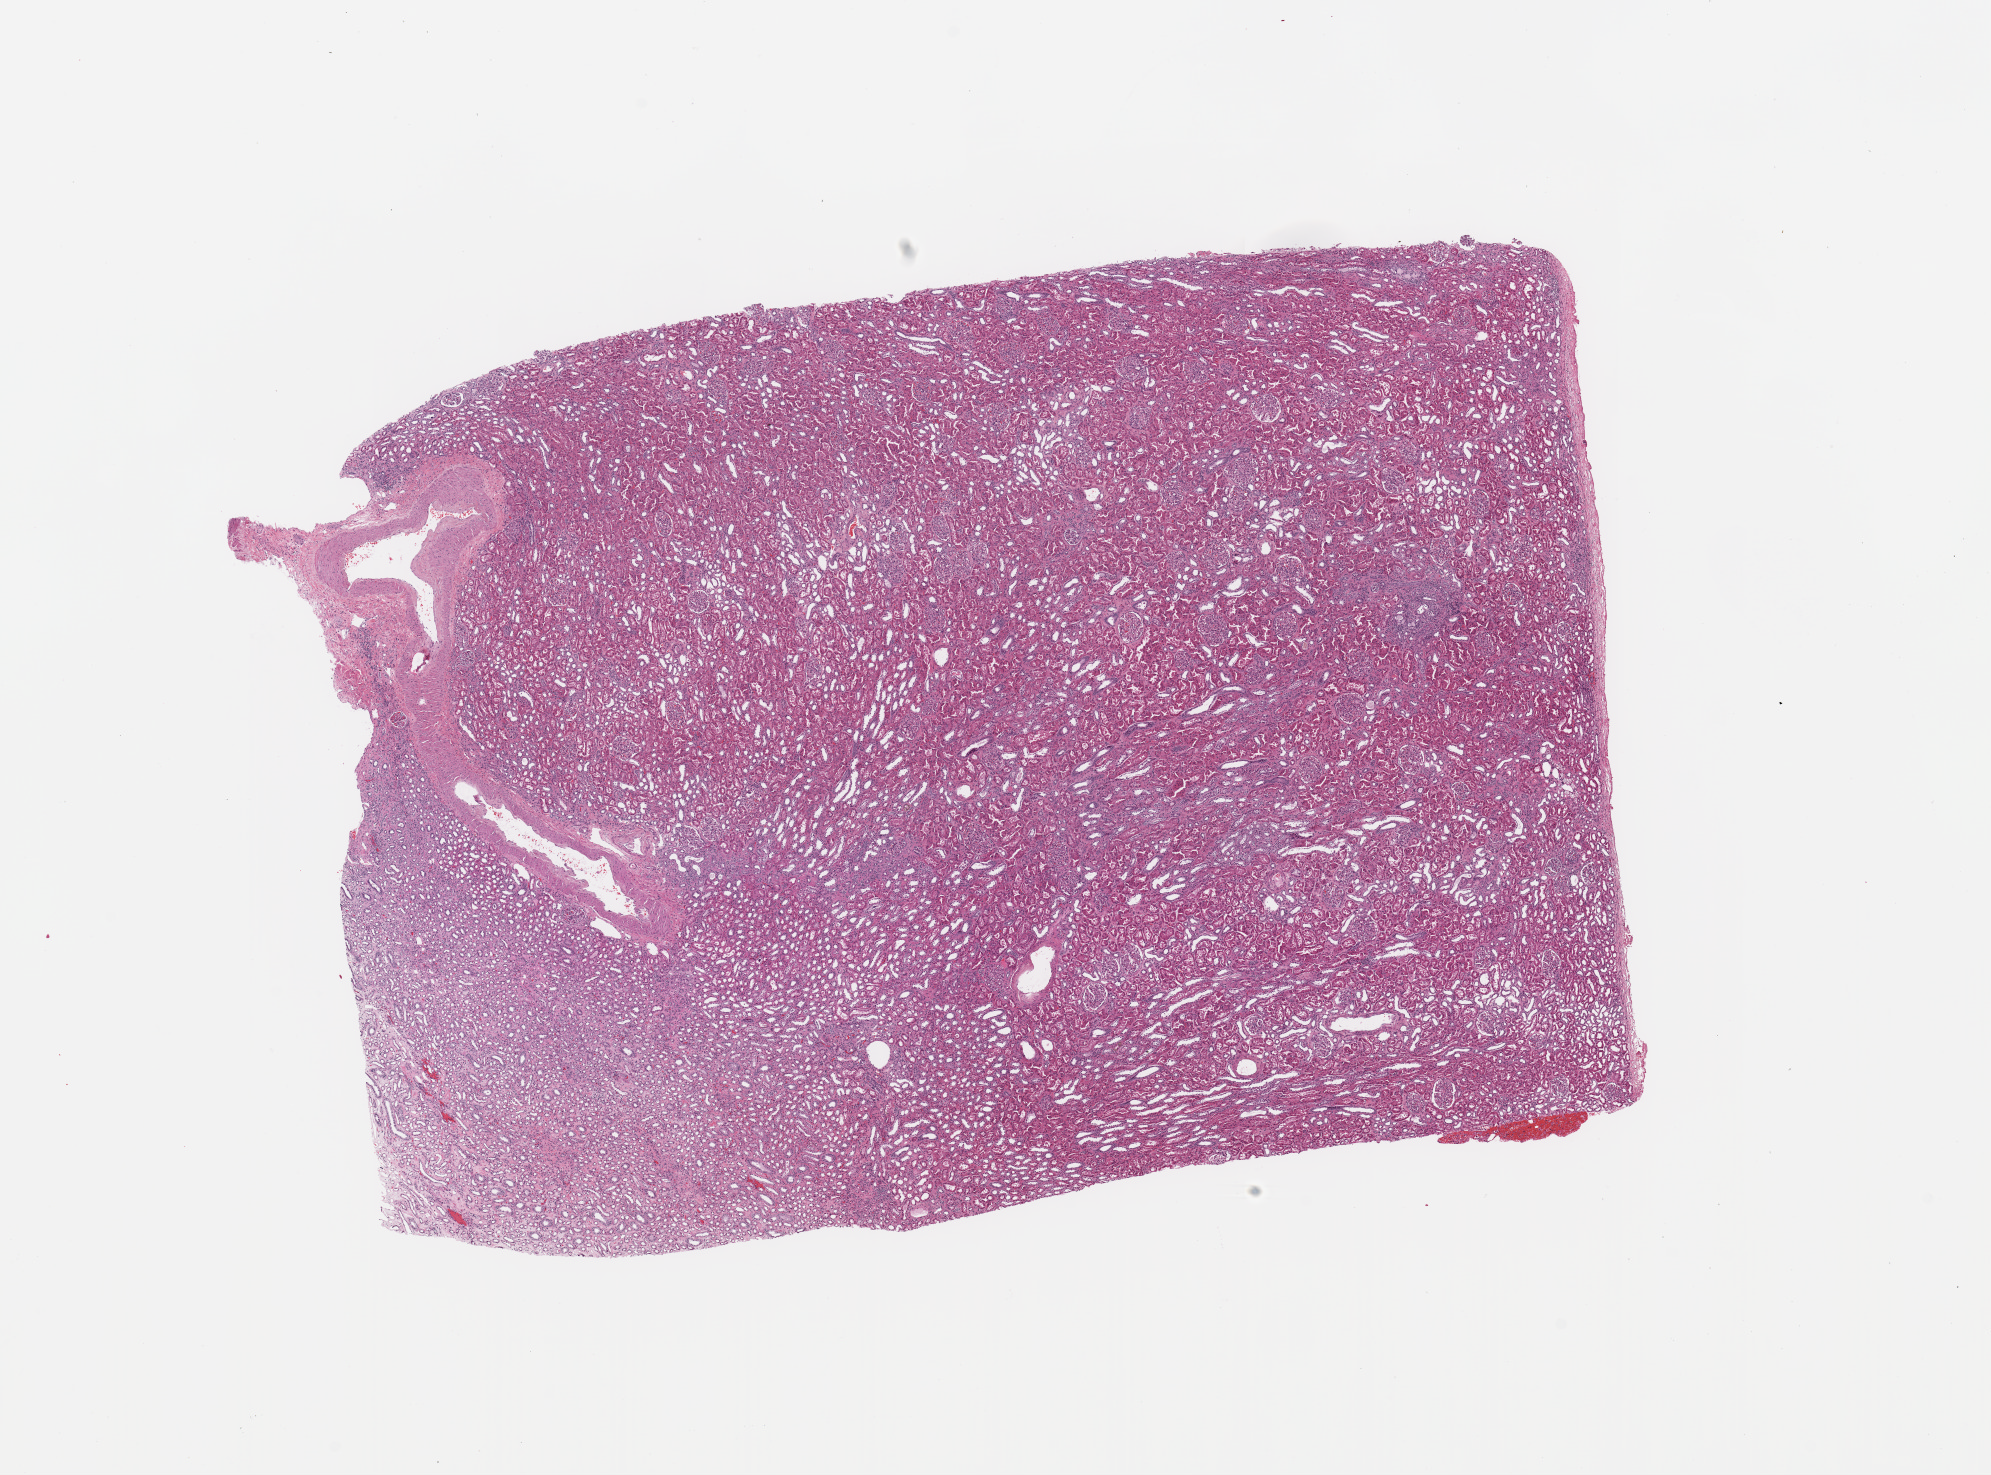
Digitized Hematoxylin and eosin (H&E) stained tissue section (whole slide), shown as a low-resolution overview of the whole scanned area (about 15.8 x 11.7 mm, from a 20x scan), normal (non-tumour) tissue sample, kidney. Male, 55 y/o.
This section: normal (non-tumour) tissue from the same patient. Patient diagnosis: Renal cell carcinoma, NOS.